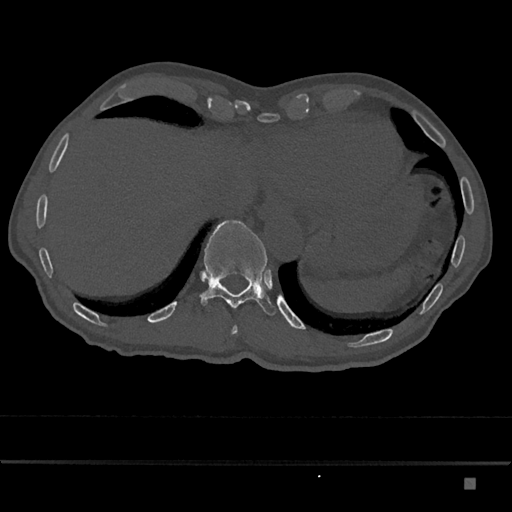
CT including the spine, one axial slice. Slice 684 of 797 in the series (ordered by position). Reconstruction kernel Br40s/3. 120 kVp. Bone window (W 1800 / L 400 HU). 512 × 512 image matrix, field of view 390 × 390 mm. Patient: male, 72 years. From the clinical record (not read from this slice): primary cancer: prostate.
Structures marked on this image (semi-automatically segmented with operator editing):
- T10 vertebra: bounding box (x1, y1, x2, y2) in pixels: (231, 325, 238, 335)
- T11 vertebra: (200, 220, 276, 316)